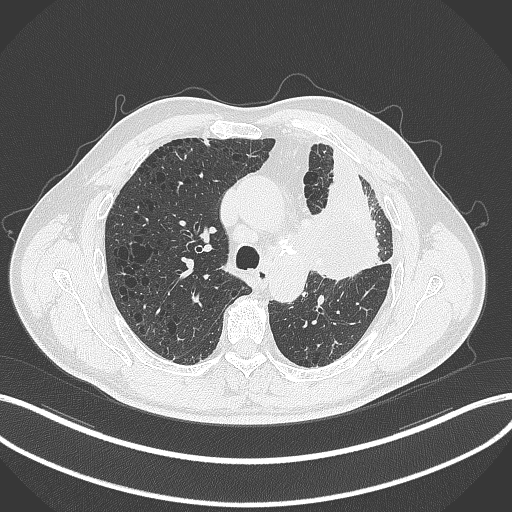
Chest CT, one axial slice. Position 213 of 297 along the scan axis. 120 kVp. Lung window (W 1500 / L -600 HU). 512 × 512 image matrix, field of view 400 × 400 mm. Patient: male, 68 years. From the clinical record (not read from this slice): clinical TNM (as recorded): T3 N3 M1.
Outlined on this slice (rectangle marked by the reading radiologist):
- lung tumour (recorded histology: adenocarcinoma): bounding box (x1, y1, x2, y2) in pixels: (306, 189, 387, 286)